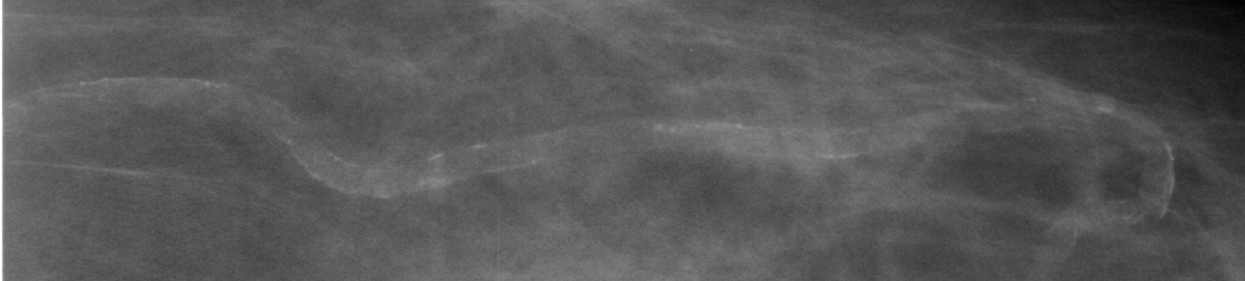
Crop from a digitized film mammogram around one marked abnormality, left breast, CC view, BI-RADS breast density category 2 (scale 1–4).
- Marked abnormality: calcifications, morphology vascular; BI-RADS assessment category 2; subtlety rating 4 on a 1 (subtle) to 5 (obvious) scale; benign without callback (not worked up further).